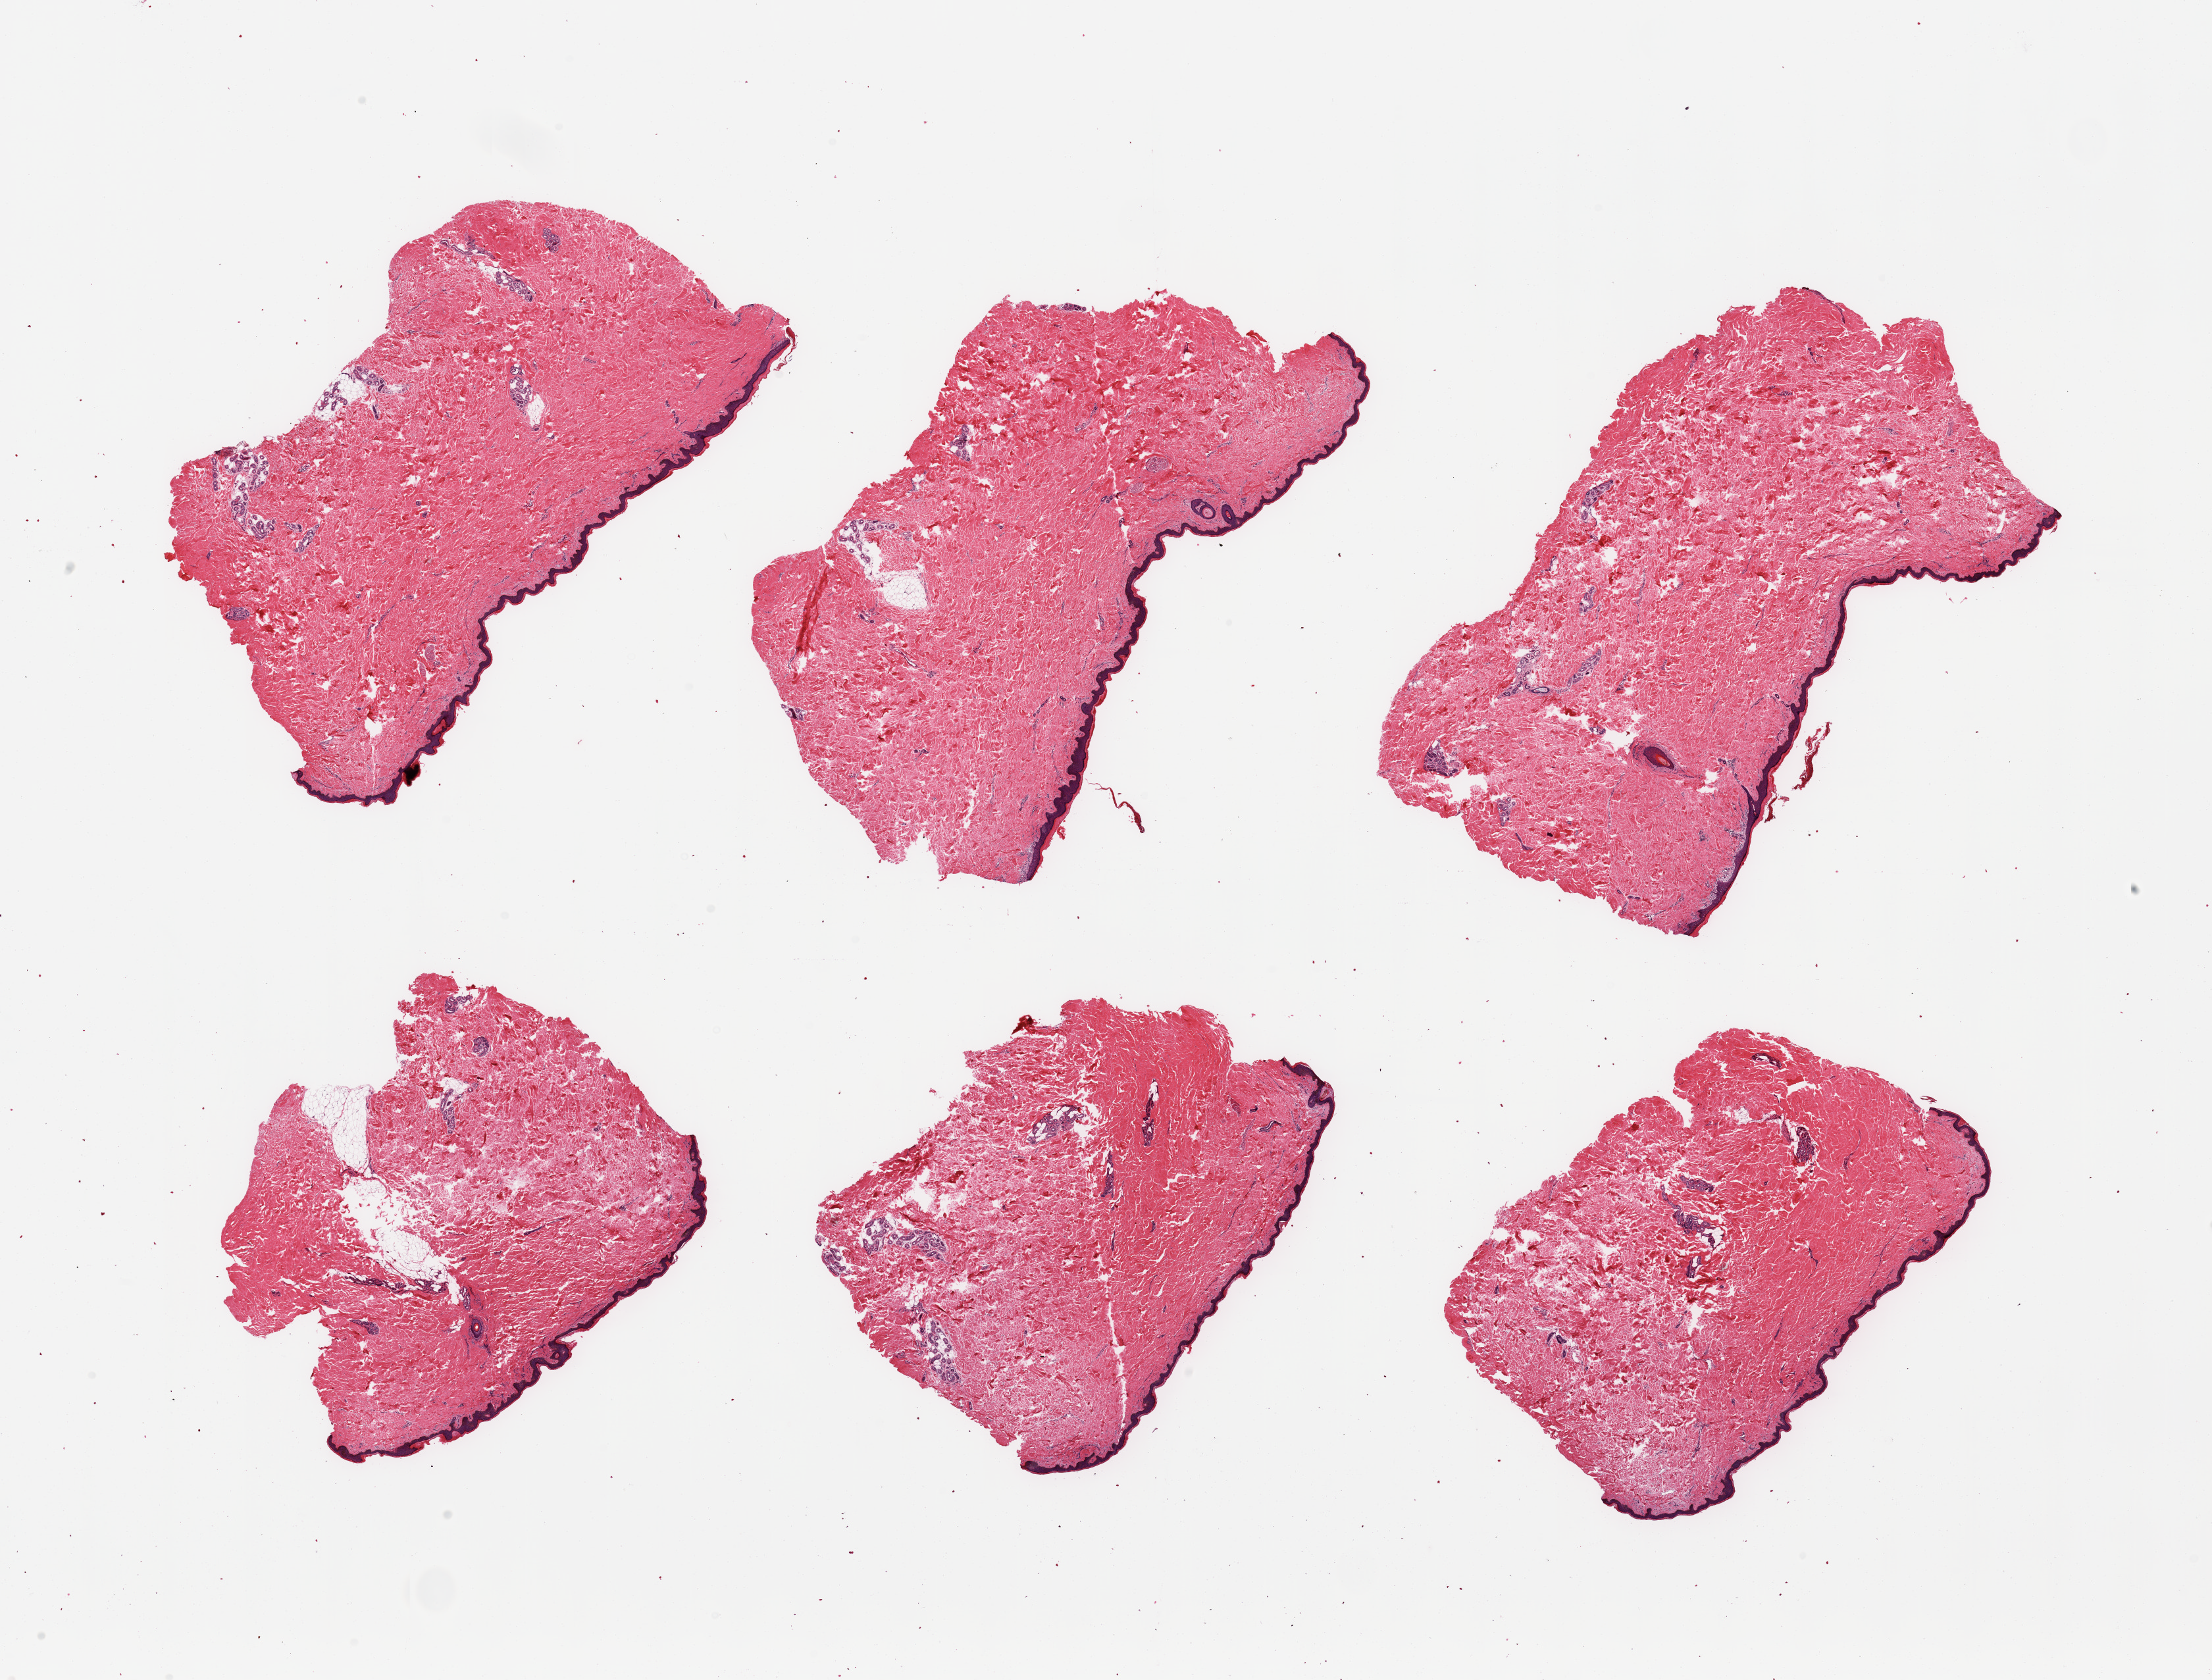
Whole-slide image, H&E stain, whole scanned area (about 26.6 x 20.2 mm, acquisition: 20x scan) shown as a low-resolution overview. PAXgene-fixed, paraffin-embedded tissue. Target tissue: skin of suprapubic region. Donor tissue sample.
Reviewer comment on this tissue sample: 6 pieces; well trimmed hair bearing skin; periadnexal fat.